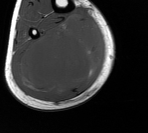
MRI of an extremity soft-tissue mass, one axial slice; position 61 of 76 along the scan axis; MR volume resampled by the dataset authors to the PET/CT grid (not the native acquisition matrix); 148 × 133 image matrix, field of view 145 × 130 mm. Male patient. Case-level facts recorded for this patient, not image findings: histological type: liposarcoma - round cell; grade: high; site of the primary tumour: right calf.
Structures marked on this image (expert contour drawn on MRI and transferred to this co-registered scan by the dataset authors):
- gross tumour volume (mass): bounding box (x1, y1, x2, y2) in pixels: (13, 17, 103, 97)